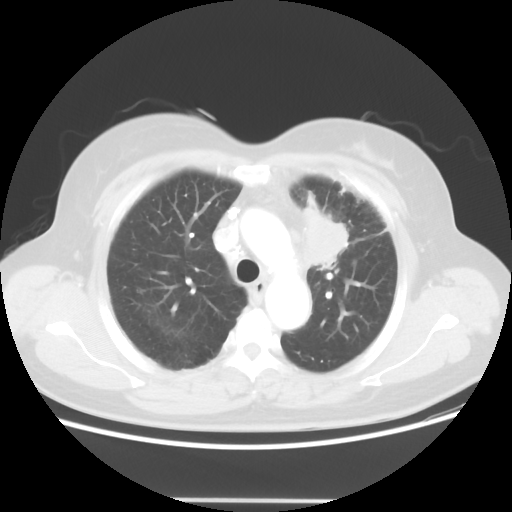
Chest CT, one axial slice. Slice 40 of 52 in the series (ordered by position). Reconstruction kernel STANDARD. 120 kVp. Lung window (W 1500 / L -600 HU). 5 mm slice thickness. 512 × 512 image matrix, field of view 382 × 382 mm. Patient: female, 52 years. Case-level facts recorded for this patient, not image findings: clinical TNM (as recorded): T2 N3 M0.
Structures marked on this image (bounding box drawn by a radiologist):
- lung tumour (recorded histology: adenocarcinoma): bounding box (x1, y1, x2, y2) in pixels: (291, 189, 352, 278)